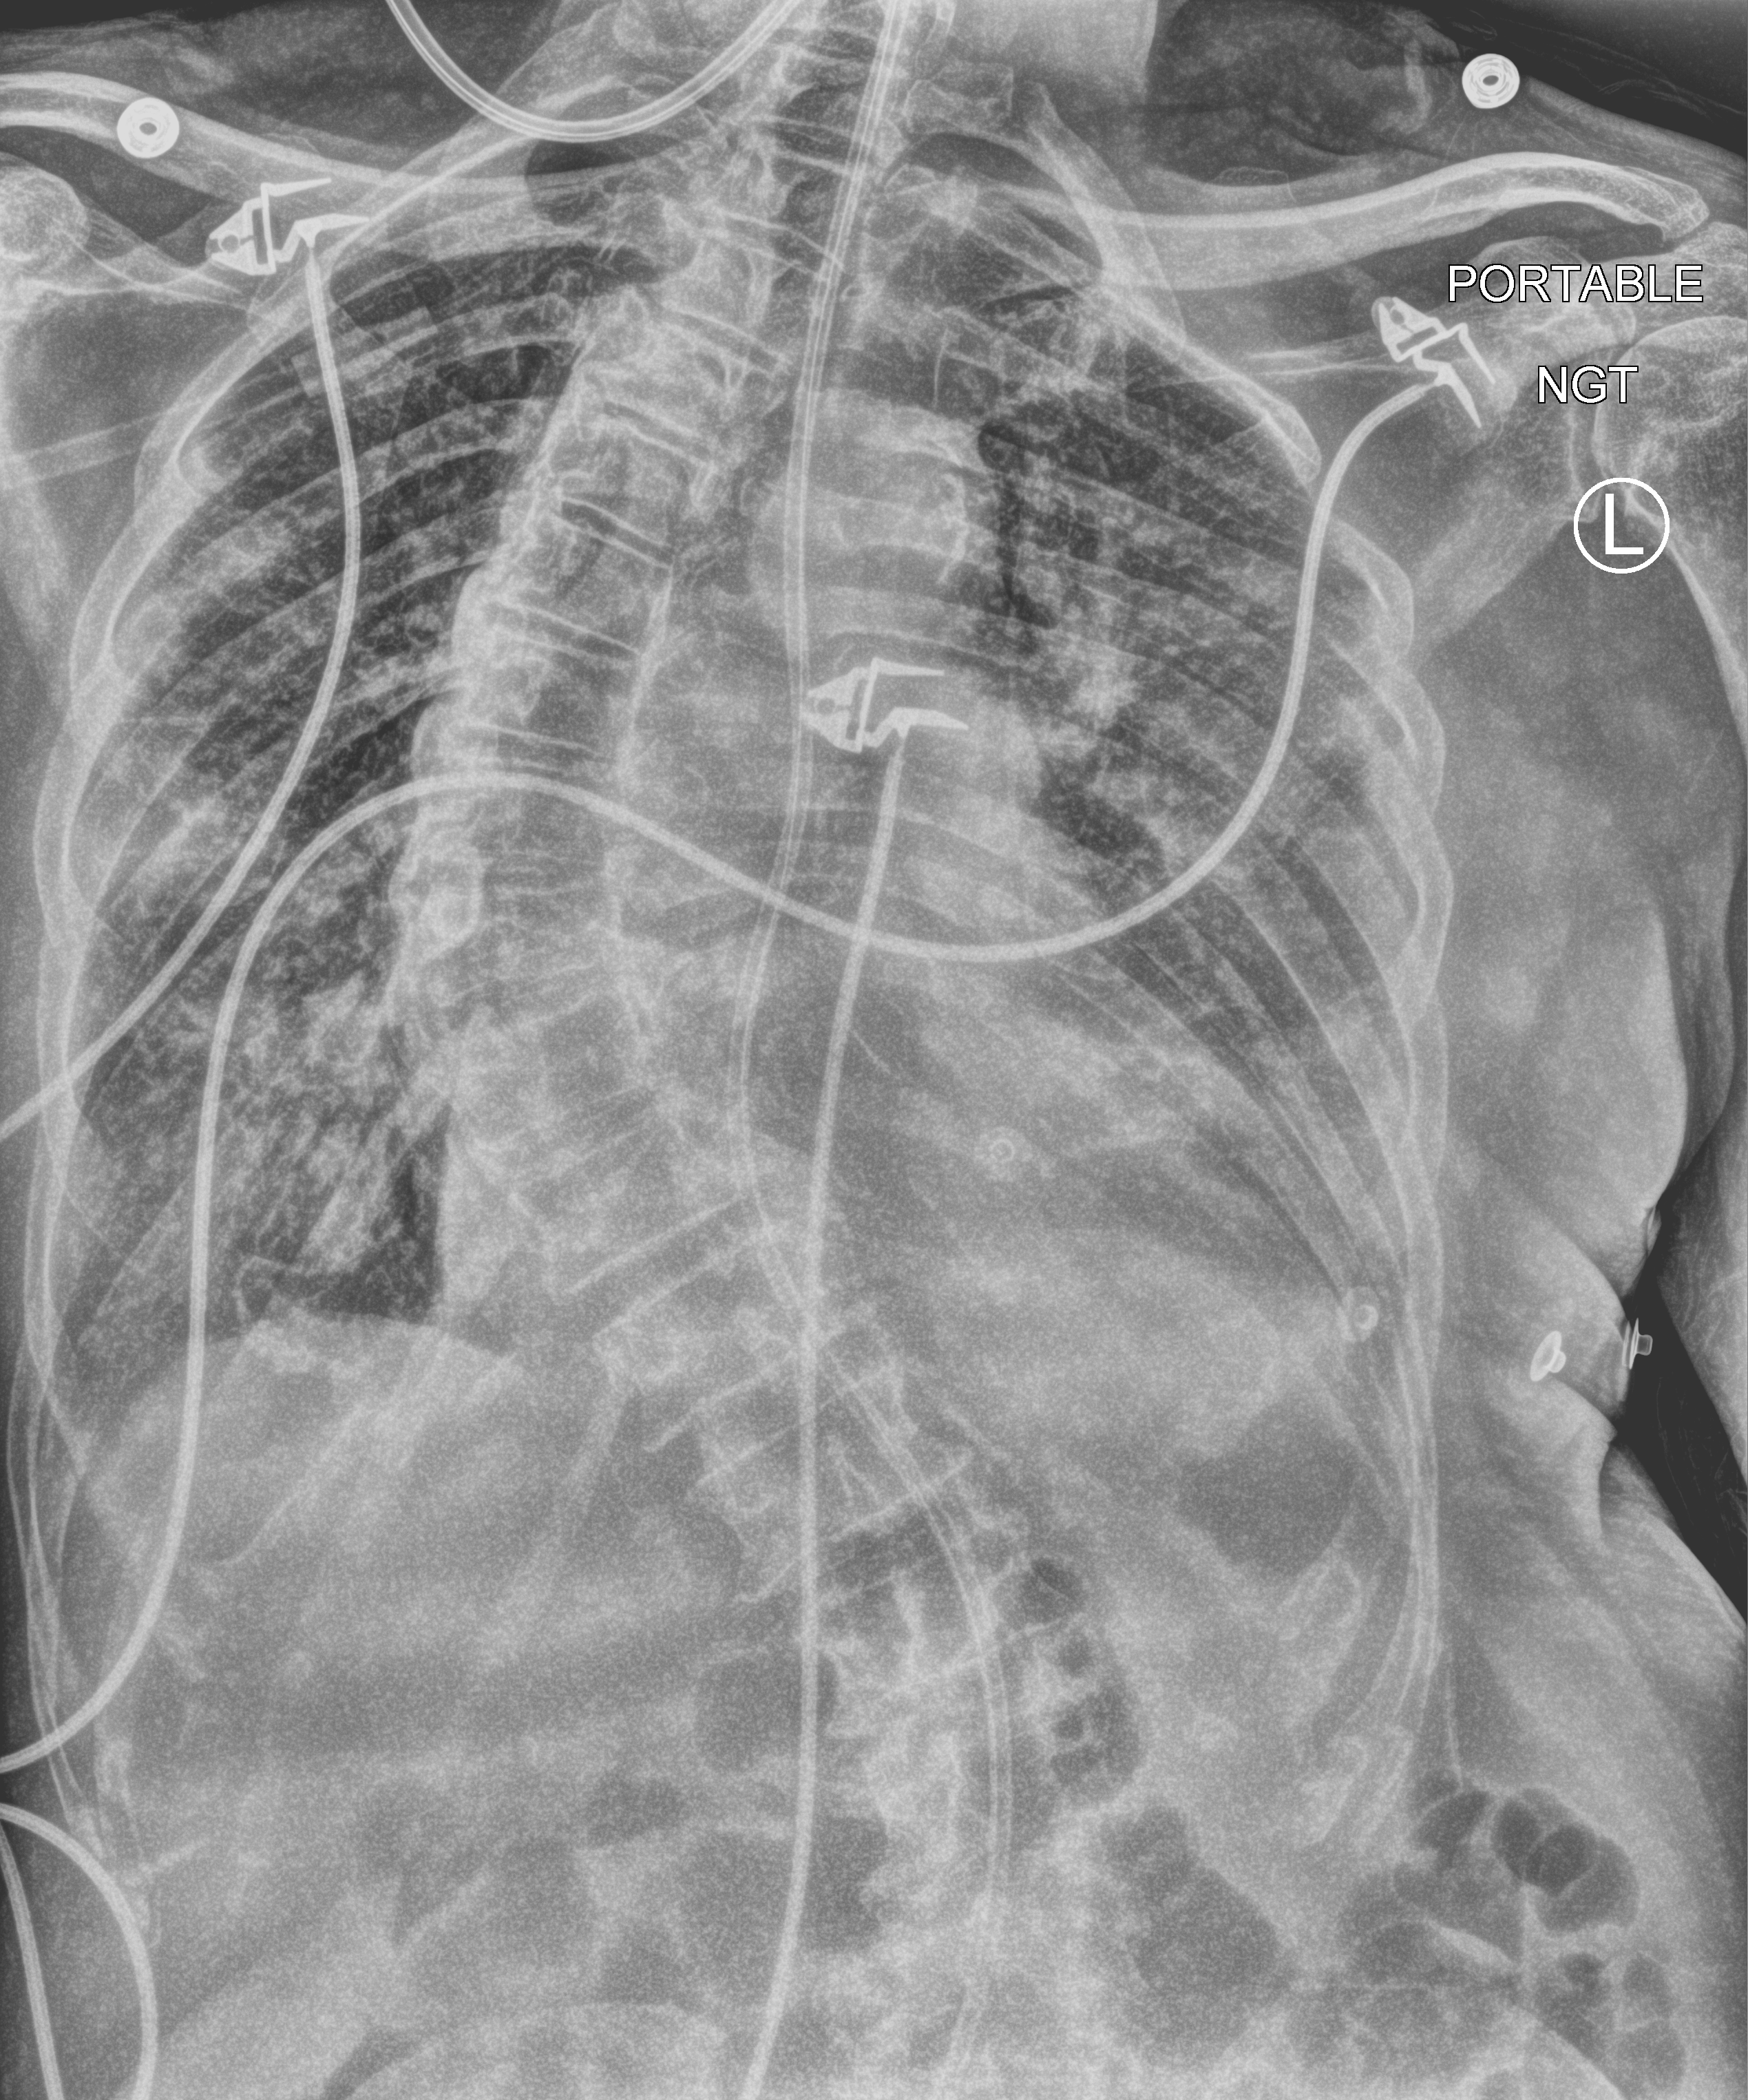
Bedside chest radiograph (computed radiography), anteroposterior (AP) projection. Patient hospitalised with COVID-19; male, aged 75–90 years.
Admission-level facts for this patient (not findings on this image; timing relative to this image not recorded):
- length of hospital stay: 12 days
- admitted to intensive care during this hospital stay: no